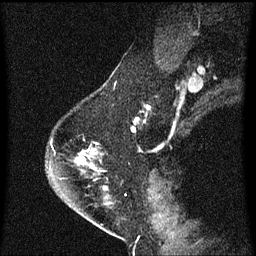
Breast MRI (dynamic contrast-enhanced), one sagittal slice; position 45 of 60 along the scan axis; dynamic contrast-enhanced series, image 2 of 3 at this slice position (ordered by acquisition); 1.5 T; TE 4.2 ms, TR 8.4 ms; 2 mm slice thickness; 256 × 256 image matrix. Female patient, age 54 years. Case-level facts recorded for this patient, not image findings: setting: breast cancer imaged before/during neoadjuvant chemotherapy; receptor status: HER2-positive.
Annotated regions visible in this slice (semi-automatically segmented with operator editing):
- analysis volume of interest (the breast-tissue region the enhancement analysis was run in; not a lesion): bounding box [x1, y1, x2, y2] px = [48, 154, 113, 211]
- tumour enhancement mask (voxels above the 70 % enhancement threshold inside the analysis volume of interest): [78, 154, 93, 169]